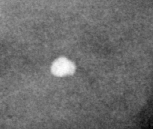
Region of interest cut from a scanned film mammogram (one marked finding), right breast, CC view.
- Calcifications, morphology round and regular / lucent center / punctate, distribution diffusely scattered; BI-RADS assessment category 2; subtlety rating 5 on a 1 (subtle) to 5 (obvious) scale; benign without callback (not worked up further).